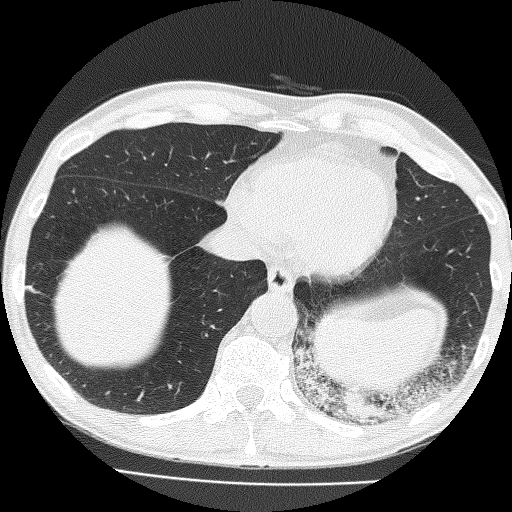
Low-dose screening chest CT, axial slice; baseline screening round; lung window (W 1500 / L -600 HU); lung (sharp) reconstruction kernel (FC51); 512 × 512 image matrix. Male participant, aged 58 years at enrolment. Current smoker at enrolment.
- Lesion marked by an expert reader, box from (x=287, y=289) to (x=432, y=436) px.
- The screening reader recorded 2 non-calcified nodules or masses ≥4 mm on this exam; which of them this box marks is not recorded.
- Participant outcome: lung cancer diagnosed 39 days after this screen — non-small cell carcinoma, left lower lobe, poorly differentiated (G3), stage IV (AJCC 6th edition), 74 mm at pathology.